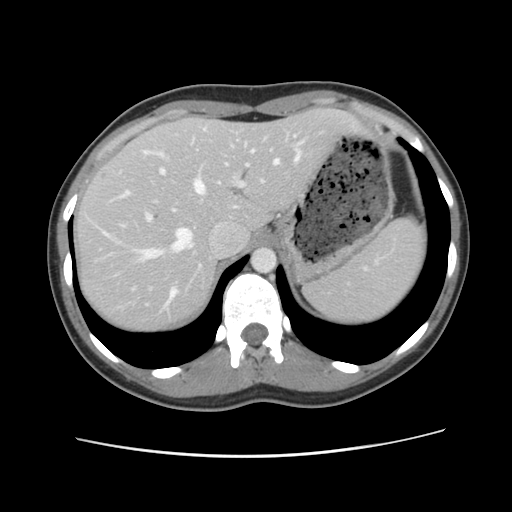
Contrast-enhanced abdominal CT, one axial slice; slice 87 of 134 in the series (ordered by position); 120 kVp; soft-tissue window (W 400 / L 40 HU); 2.5 mm slice thickness; 512 × 512 image matrix, field of view 339 × 339 mm. Female patient, age 33 years. Case-level facts recorded for this patient, not image findings: diagnosis: colorectal cancer liver metastases, imaged before liver resection; multiple liver metastases: yes; largest metastasis: 4.5 cm; disease in both lobes: yes.
Outlined on this slice (expert manual segmentation):
- hepatic veins: box from (x=105, y=143) to (x=303, y=304) px
- liver: (x=74, y=110)–(x=362, y=334)
- planned liver remnant (the part of the liver to remain after resection): (x=75, y=110)–(x=361, y=334)
- portal vein (with intrahepatic branches): (x=144, y=139)–(x=293, y=223)
- liver metastasis: (x=99, y=171)–(x=109, y=181)